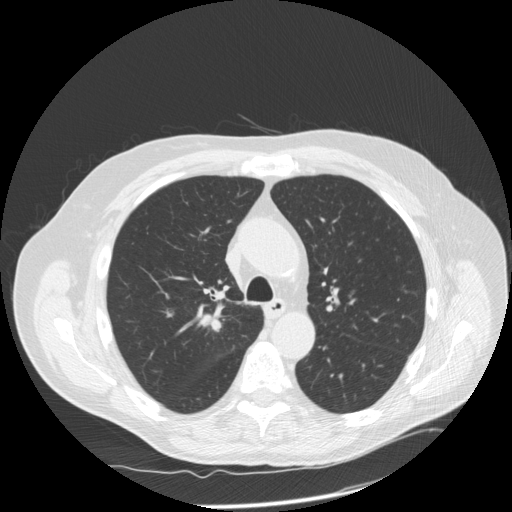
Low-dose screening chest CT, axial slice. Third annual screen. Lung window (W 1500 / L -600 HU). 2.5 mm slice thickness. Standard (soft-tissue) reconstruction kernel (STANDARD). Slice 54 of 166 in the series. 512 × 512 image matrix, field of view 390 × 390 mm. Male participant, aged 69 years at enrolment.
Lesion marked by an expert reader, bounding box (x1, y1, x2, y2) in pixels: (184, 296, 242, 346). Reader record for this screening exam (exam-level; its link to the box is not recorded): non-calcified nodule or mass ≥4 mm, right upper lobe, 18 × 17 mm, spiculated (stellate) margins, soft tissue attenuation, pre-existing on the prior screen: no. Official screen result: positive, other. Later outcome: lung cancer diagnosed 13 days after this screen — squamous cell carcinoma, NOS, right upper lobe, poorly differentiated (G3), stage IA (AJCC 6th edition), 22 mm at pathology.